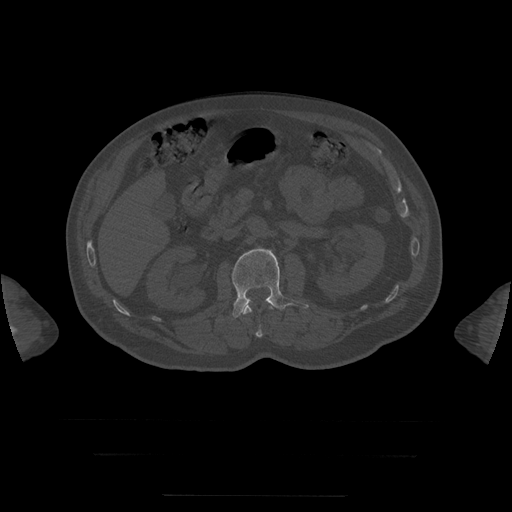
CT including the spine, one axial slice. Slice 29 of 397 in the series (ordered by position). Reconstruction kernel STANDARD. Bone window (W 1800 / L 400 HU). 1.25 mm slice thickness. 512 × 512 image matrix. Patient age 73 years. Case-level facts recorded for this patient, not image findings: primary cancer: prostate.
Annotated regions visible in this slice (semi-automatically segmented with operator editing):
- L1 vertebra: bounding box (x1, y1, x2, y2) in pixels: (243, 301, 273, 338)